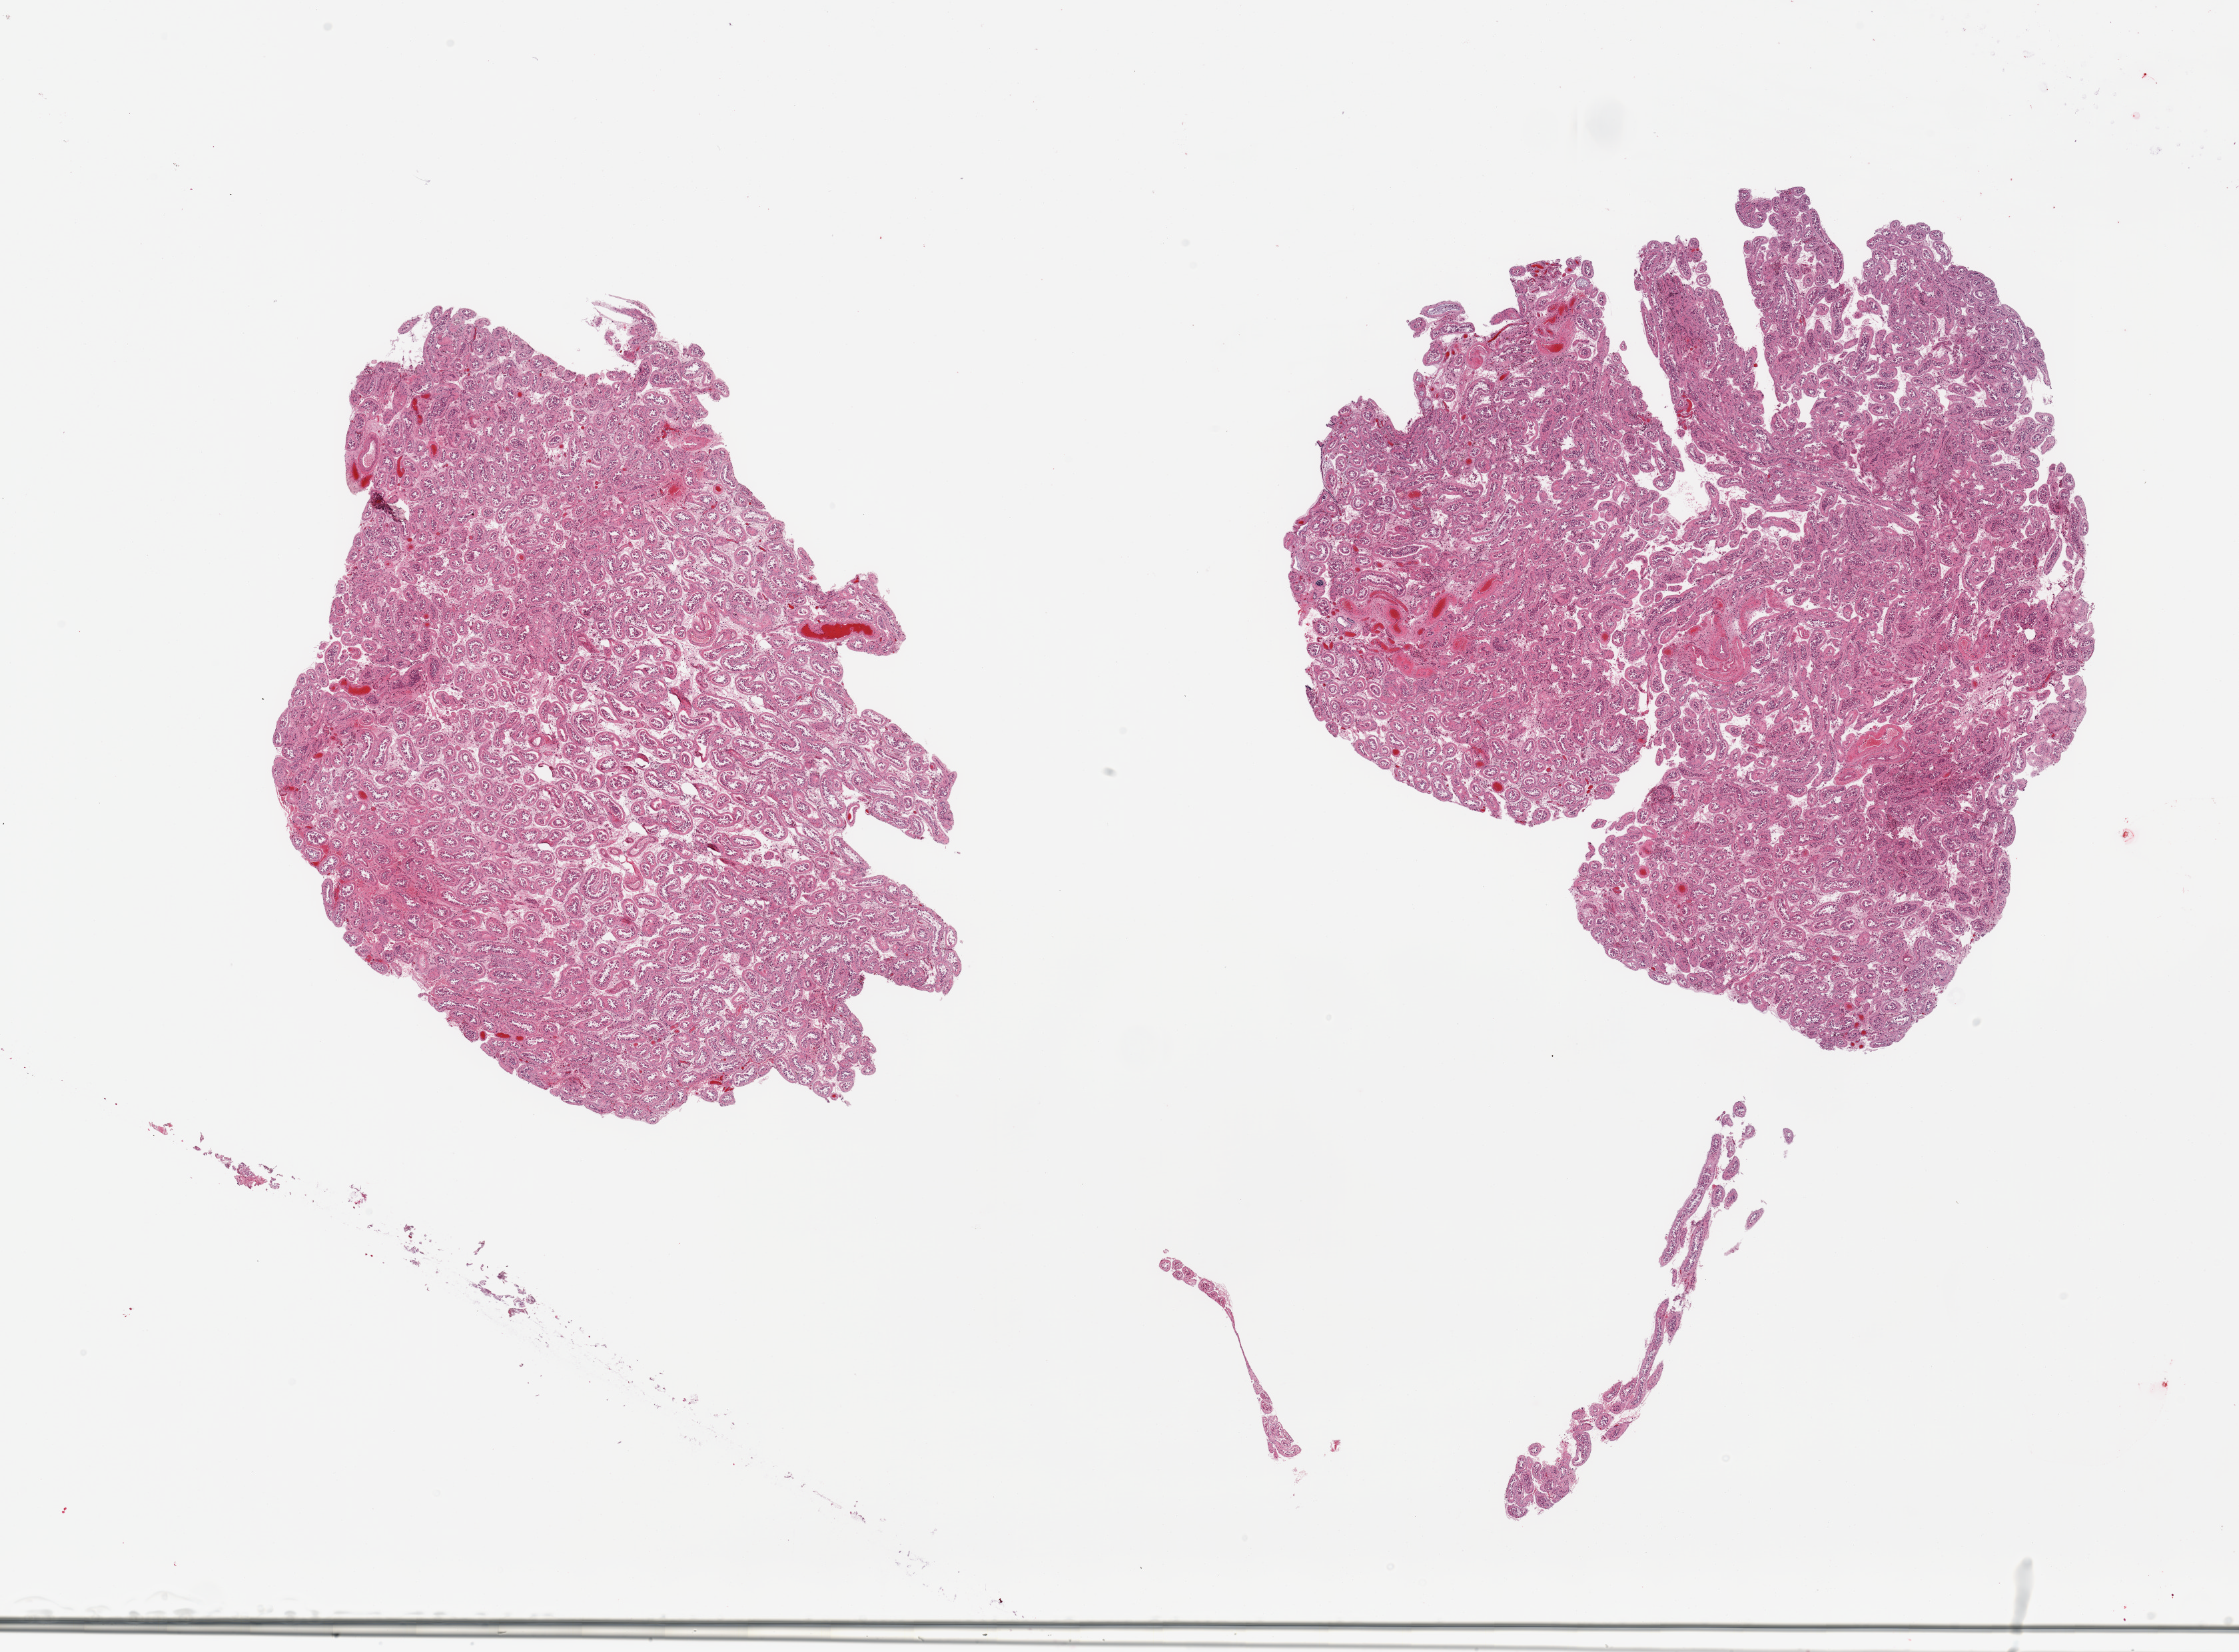
Digitized H&E-stained section, brightfield — a low-resolution overview of the entire scanned area, about 26.6 x 19.6 mm (acquisition: 20x scan); PAXgene-fixed paraffin-embedded (PFPE) section; section of testis (target tissue); tissue donor sample. Donor: male.
Review note (as recorded): 2 pieces; thickening of tubular basement membrane; lack of spermatogenesis; increase of Sertolli cells; congestion.